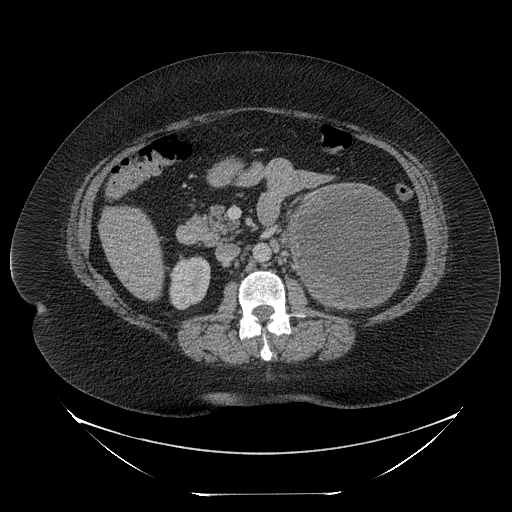
Contrast-enhanced abdominal CT, one axial slice; position 126 of 205 along the scan axis; reconstruction kernel STANDARD; 120 kVp; intravenous contrast given; soft-tissue window (W 400 / L 40 HU); 2.5 mm slice thickness; 512 × 512 image matrix, field of view 500 × 500 mm. Female patient, age 53 years. Case-level facts recorded for this patient, not image findings: diagnosis: adrenocortical carcinoma; tumour side: left adrenal; tumour size at pathology: 17 cm; Ki-67 index: 20 %; stage (as recorded): 3.
Structures marked on this image (semi-automatically segmented with operator editing):
- mass: bounding box [x1, y1, x2, y2] px = [293, 187, 408, 307]